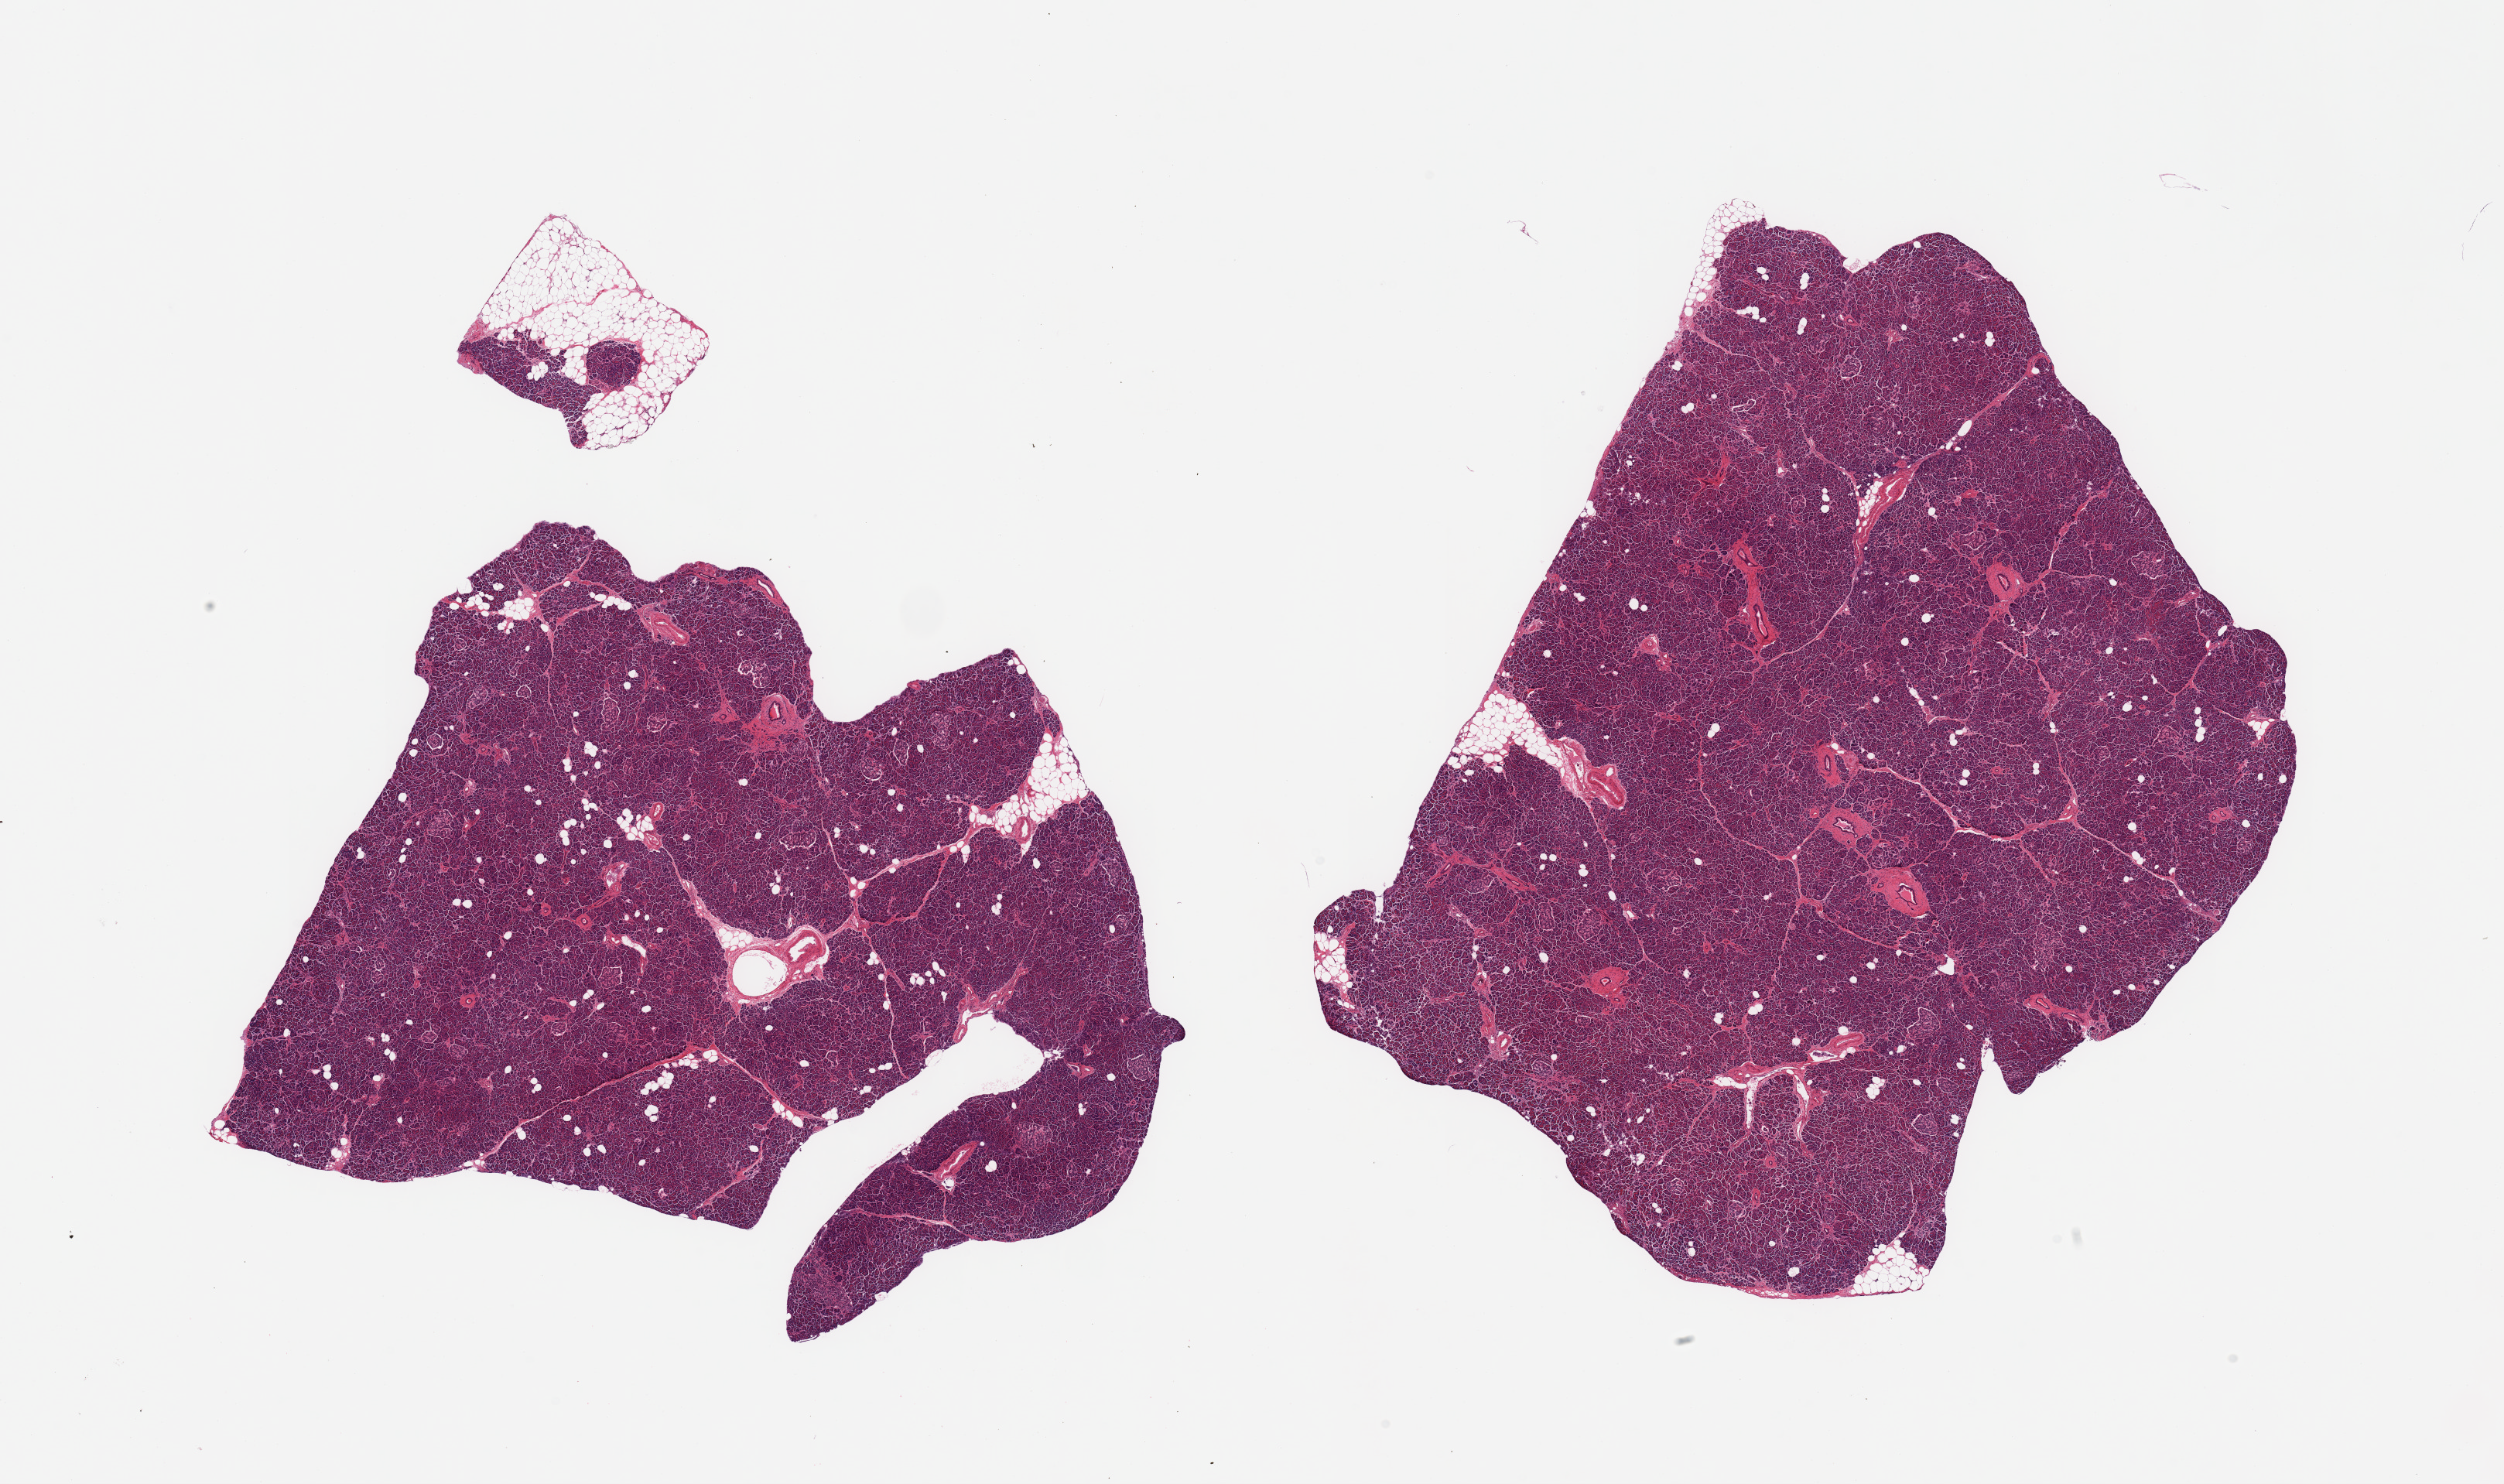
Whole-slide image, haematoxylin and eosin stain, brightfield, low-resolution overview of the scanned area, about 25.6 x 15.2 mm (slide scanned at 20x); PAXgene-fixed, paraffin-embedded tissue; target tissue: pancreas; tissue donor sample. Donor: male.
• pathologist's review note for this sample: 2 pieces; includes minimal fat, islets are well visualized